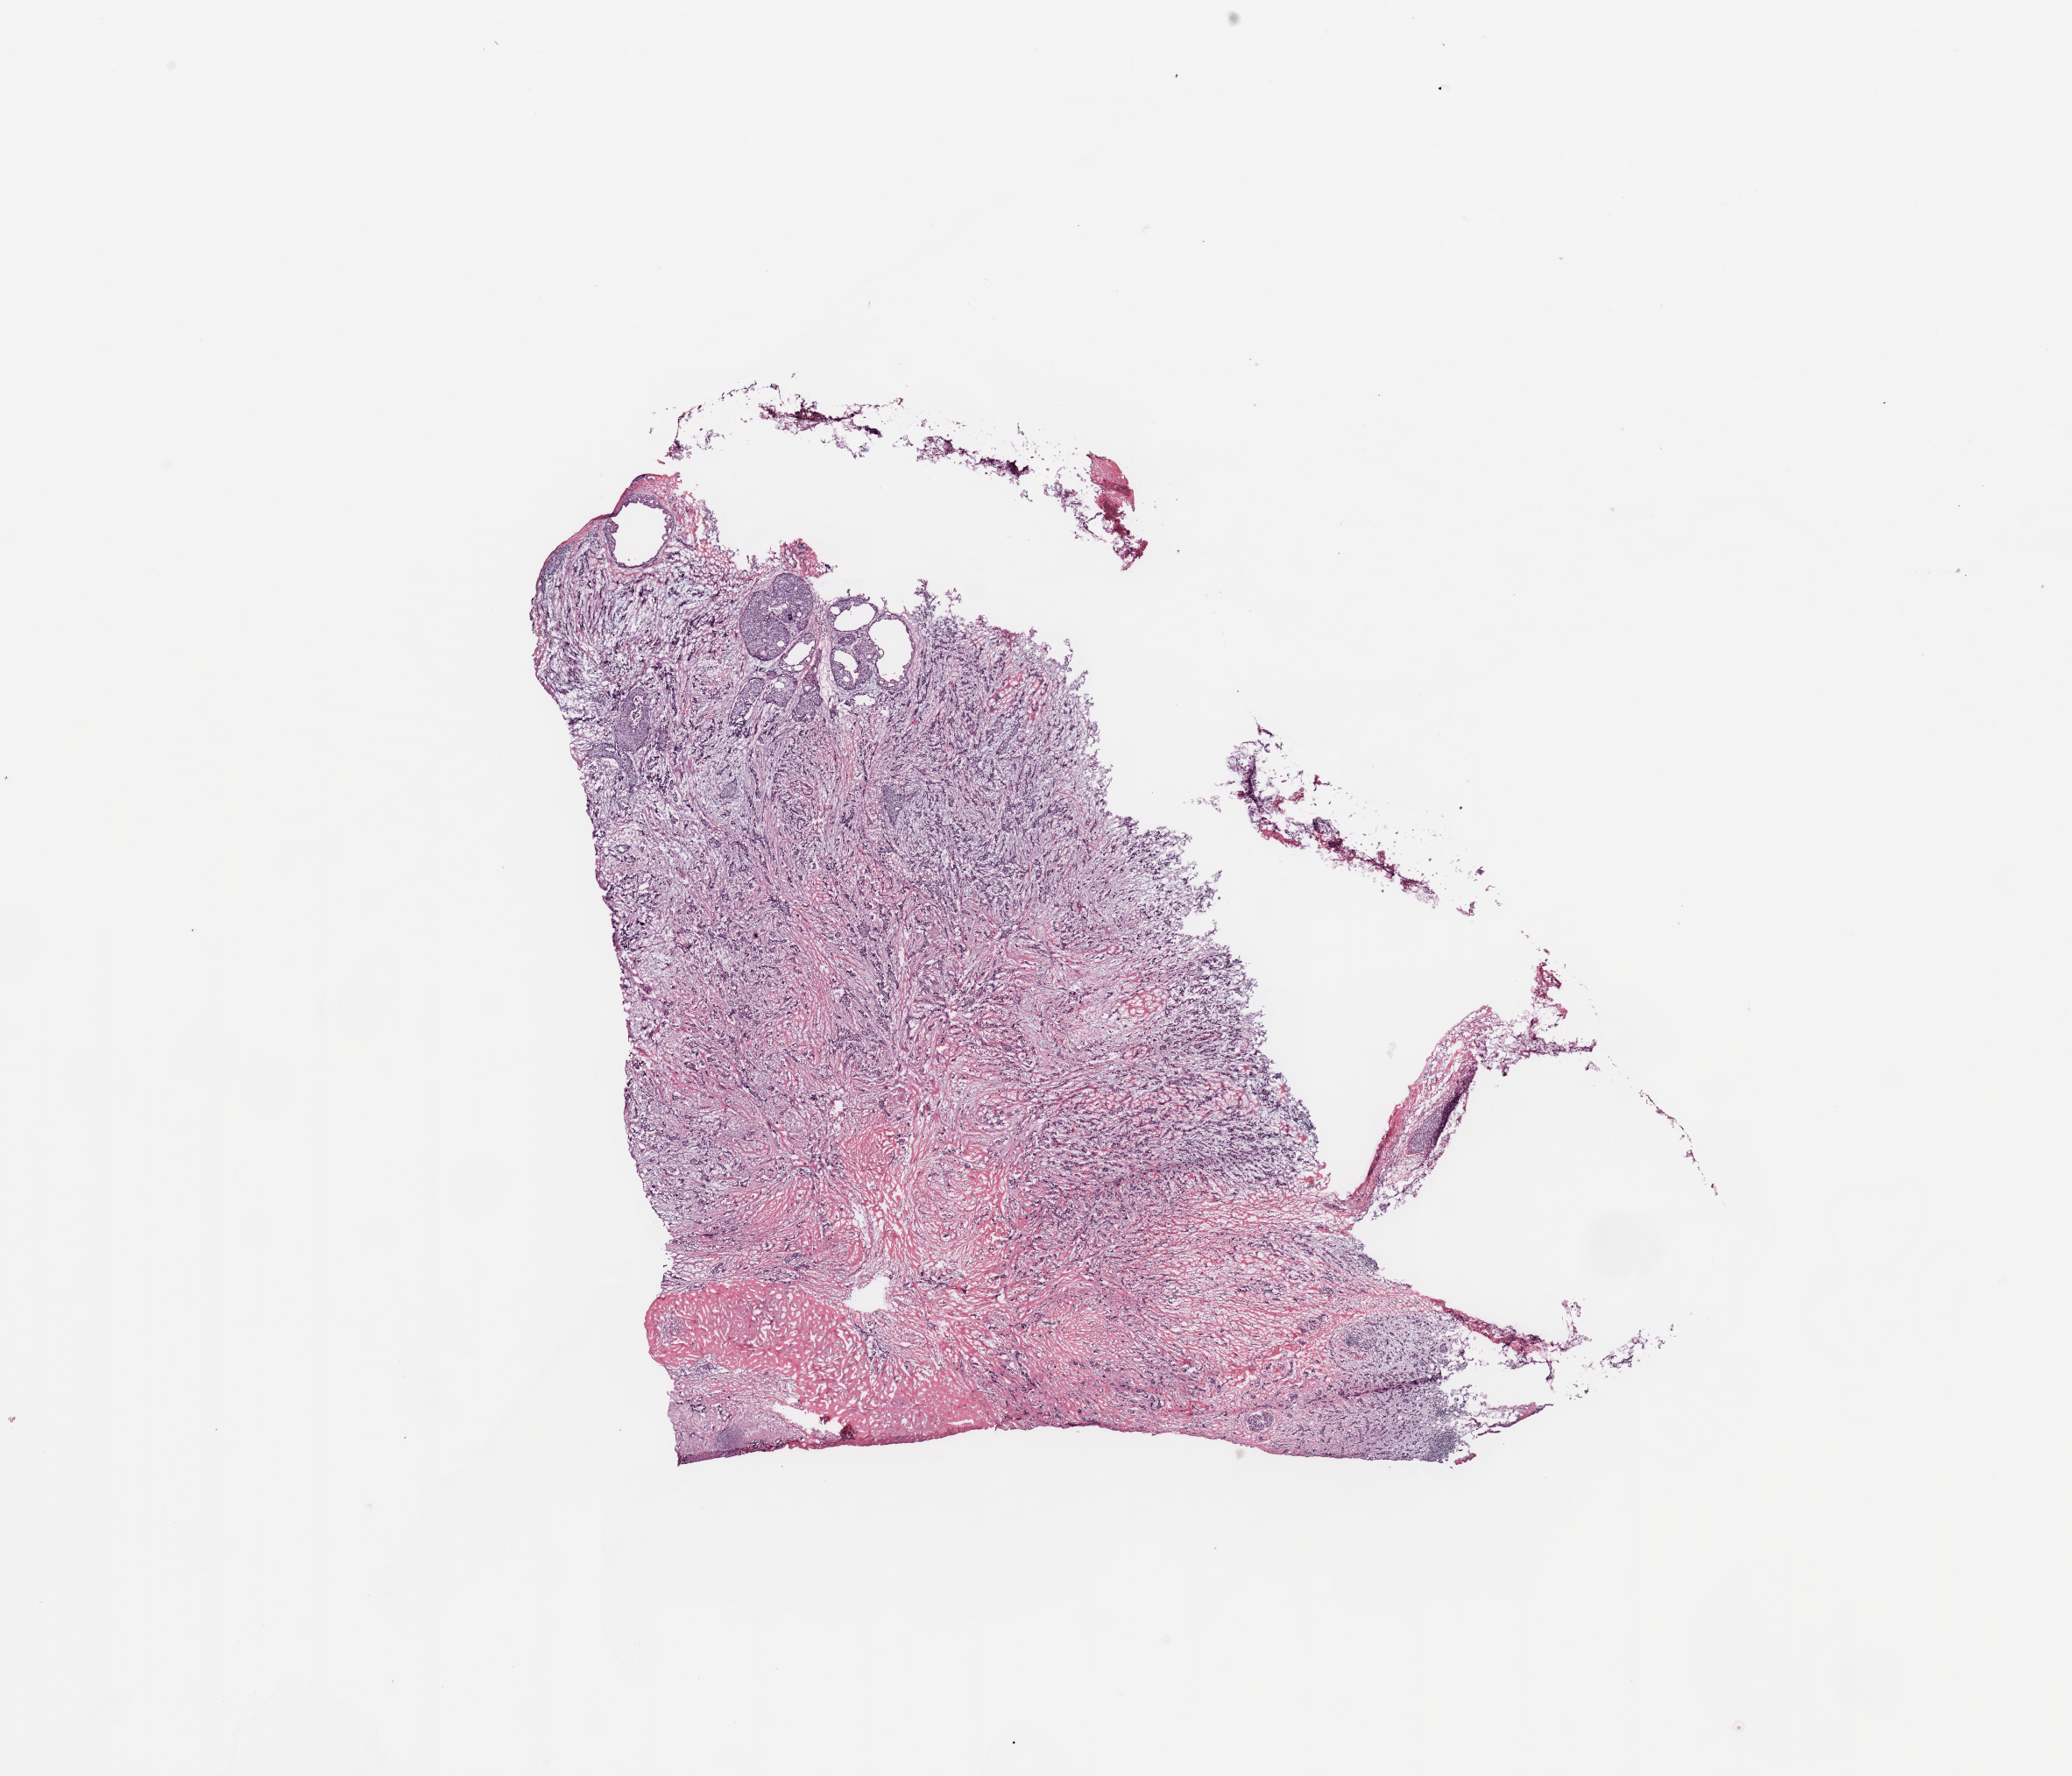
Whole-slide histology image, H&E-stained — low-resolution overview of the scanned area, about 18.7 x 16.0 mm (slide scanned at 20x); breast, tissue type not recorded.
• patient diagnosis (cohort enrolment): breast cancer (breast)